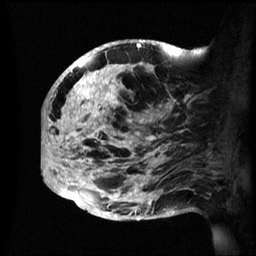
Breast MRI (dynamic contrast-enhanced), one sagittal slice. Slice 24 of 60 in the series (ordered by position). Dynamic contrast-enhanced series, image 2 of 3 at this slice position (ordered by acquisition). 1.5 T. TE 4.2 ms, TR 8.4 ms. 2.4 mm slice thickness. 256 × 256 image matrix, field of view 230 × 230 mm. Female patient, age 48 years.
Outlined on this slice (semi-automatically segmented with operator editing):
- analysis volume of interest (the breast-tissue region the enhancement analysis was run in; not a lesion): bounding box [x1, y1, x2, y2] px = [43, 41, 195, 221]
- tumour enhancement mask (voxels above the 70 % enhancement threshold inside the analysis volume of interest): [43, 41, 179, 208]